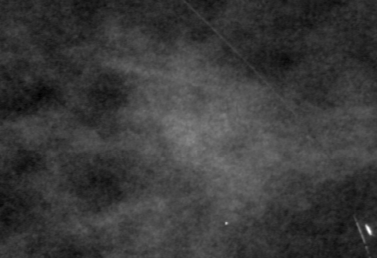
Region of interest cut from a scanned film mammogram (one marked finding); left breast; CC view; BI-RADS breast density category 3 (scale 1–4).
Finding: mass, shape irregular, margins ill defined; BI-RADS assessment category 4; subtlety rating 1 on a 1 (subtle) to 5 (obvious) scale; pathology result (as recorded, not read from the image): malignant.